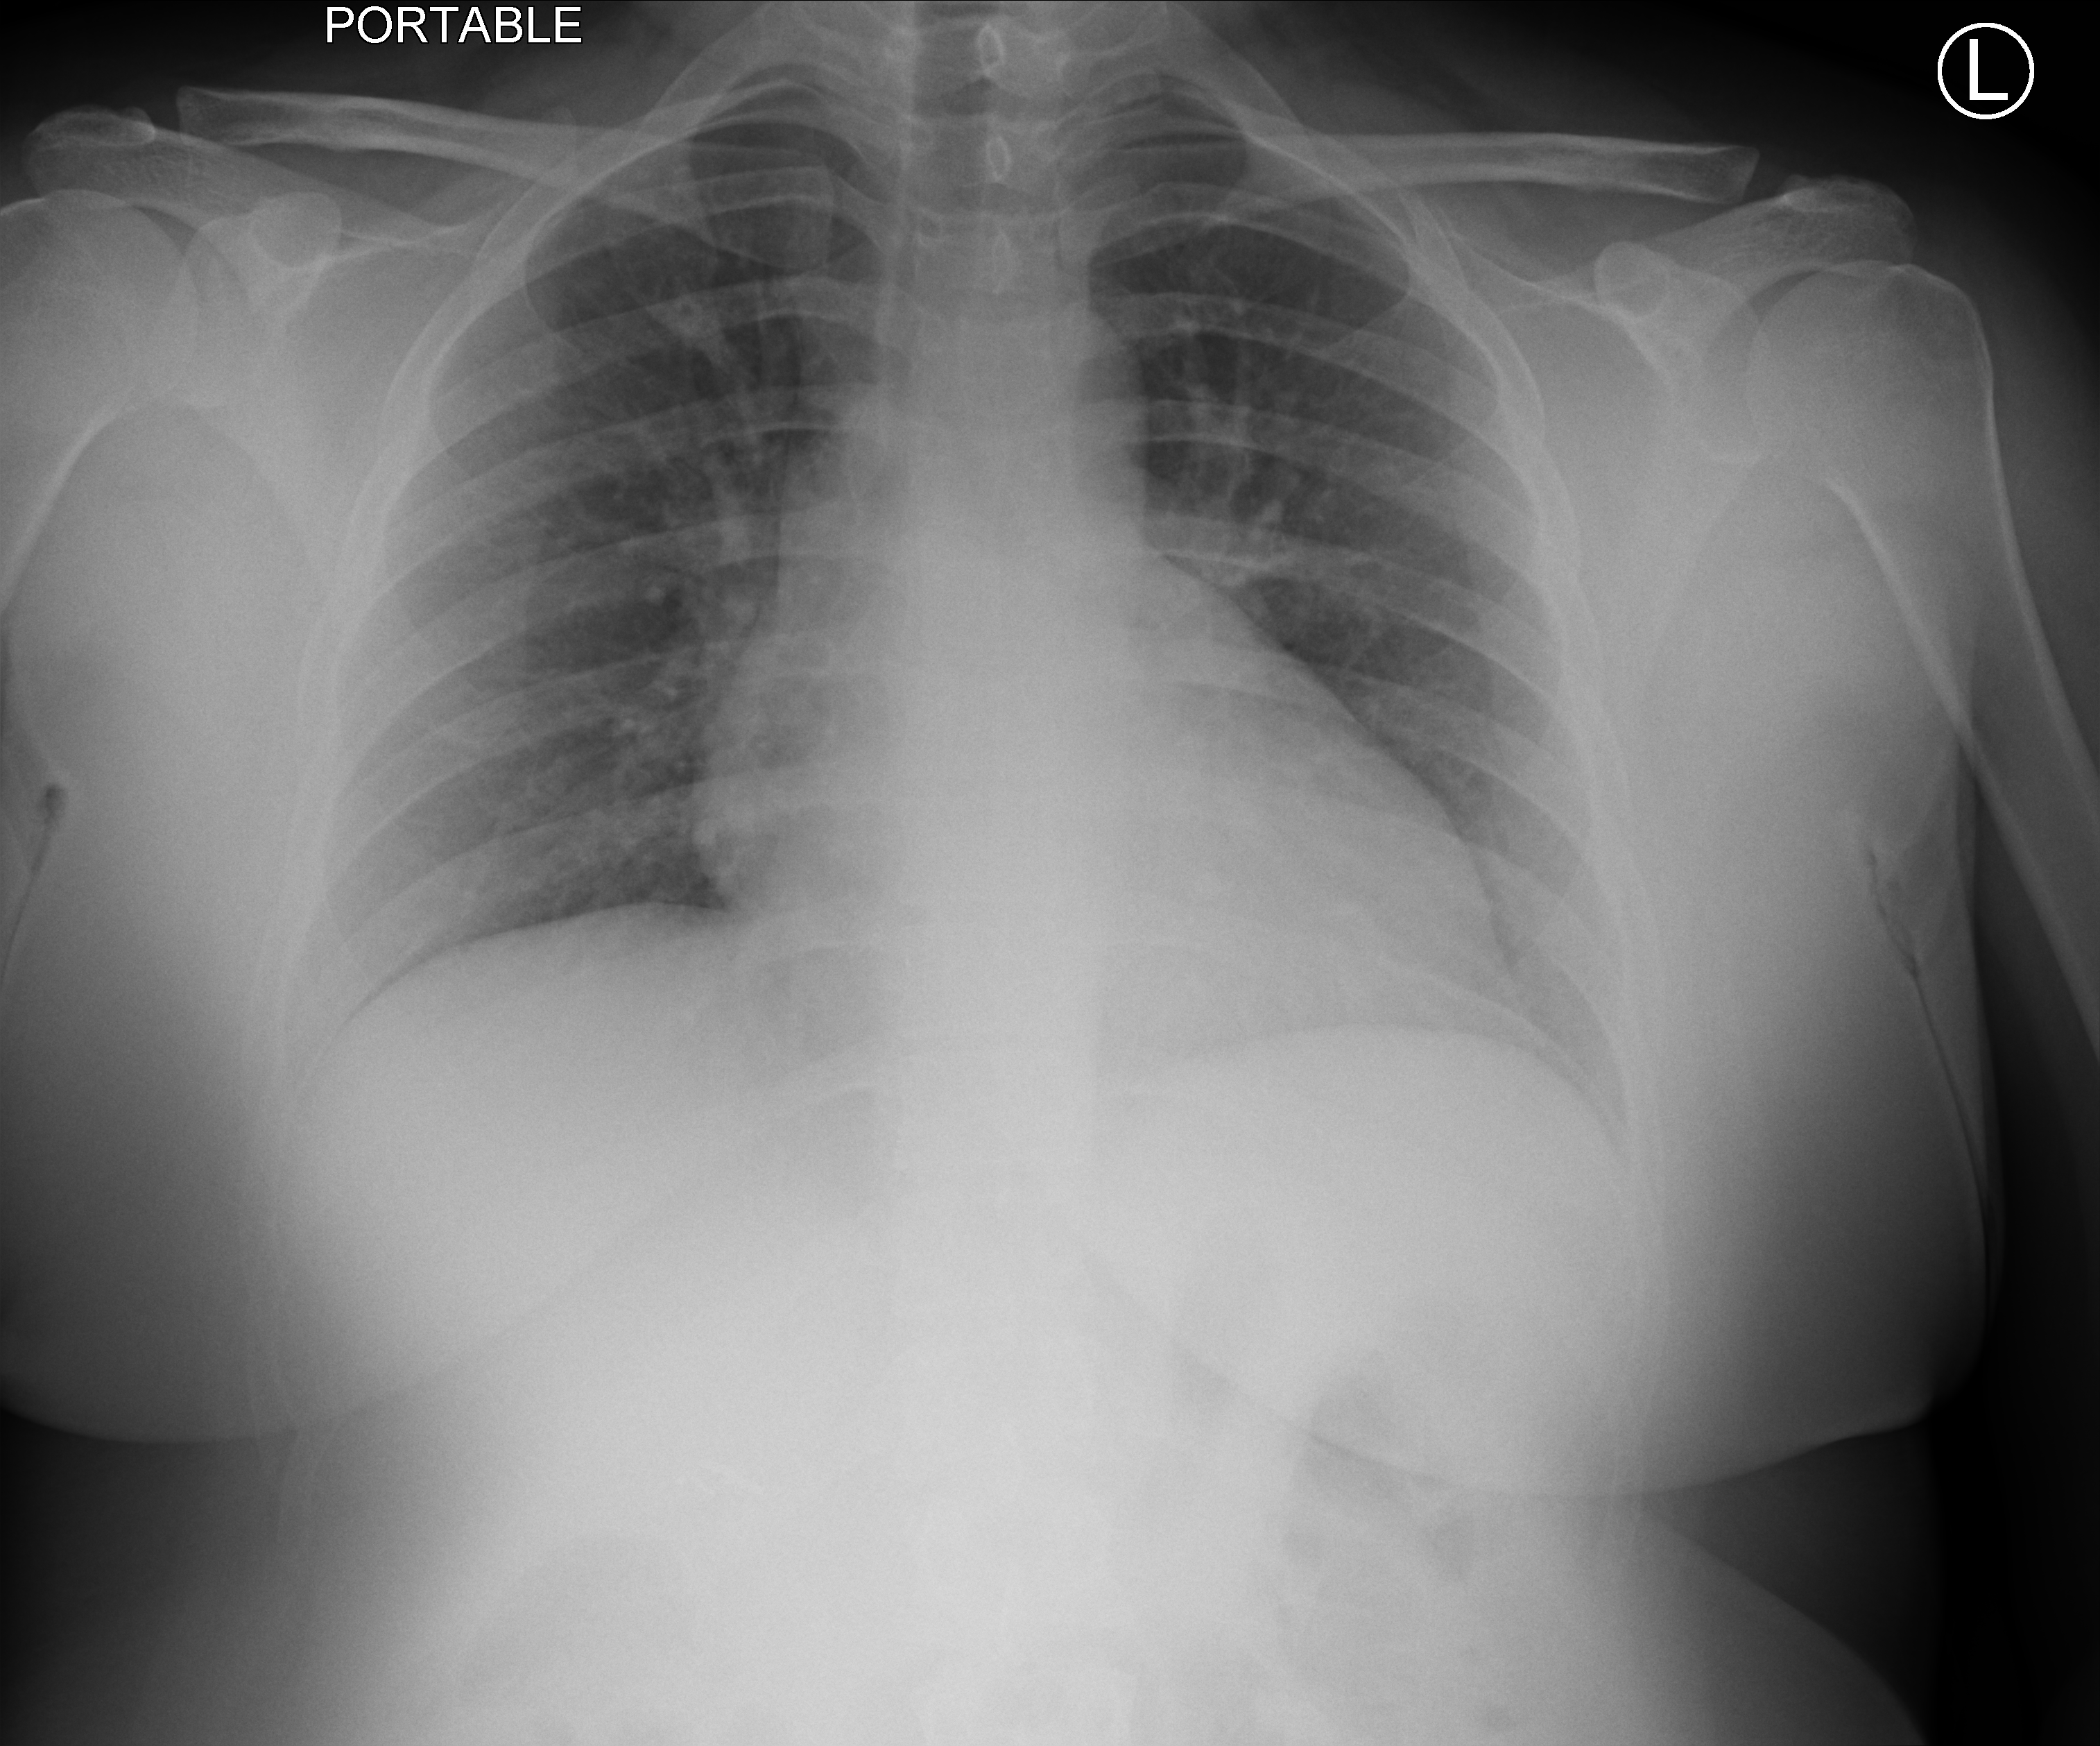
Chest X-ray (portable); anteroposterior (AP) projection. Patient hospitalised with COVID-19; female, aged 18–59 years.
From the hospital-stay record, not from the radiograph (when in the stay this image was taken is not recorded): length of hospital stay: 10 days; mechanically ventilated during this hospital stay: no; hypertension (admission record): no.